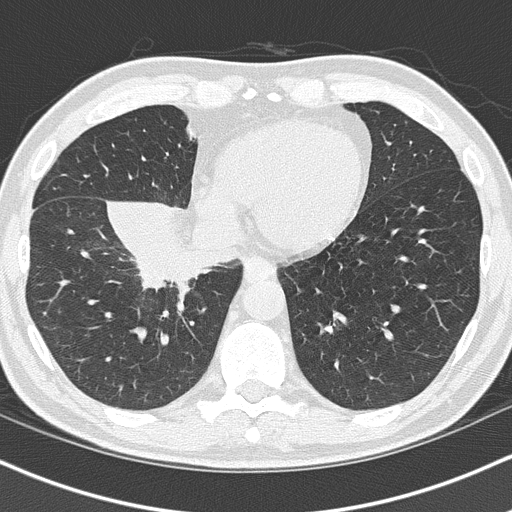
Chest CT (low-dose screening protocol), one axial image, first (baseline) screen, lung window (W 1500 / L -600 HU), 2 mm slice thickness, lung (sharp) reconstruction kernel (B50f), 120 kVp. Male participant, aged 55 years at enrolment. Current smoker at enrolment.
Expert-annotated lung lesion, box from (x=117, y=221) to (x=244, y=318) px. Reader record for this screening exam (exam-level; its link to the box is not recorded): non-calcified nodule or mass ≥4 mm, right lower lobe, 6 × 5 mm, spiculated (stellate) margins, soft tissue attenuation. Official screen result: positive, change unspecified: nodule(s) >= 4 mm or enlarging nodule(s), mass(es), or other non-specific abnormalities suspicious for lung cancer.